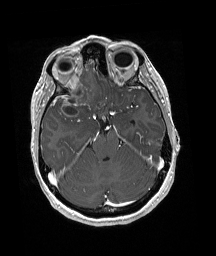
Brain MRI from a brain-tumour surgery series, one axial slice; position 124 of 192 along the scan axis; T1-weighted post-contrast; 1 mm slice thickness; 216 × 256 image matrix. From the clinical record (not read from this slice): histopathology: Oligodendroglioma; WHO grade: 3; IDH mutation: yes; tumour location: Right Frontal.
Annotated regions visible in this slice (expert manual segmentation):
- tumour: bounding box <53,74,97,117> (left, top, right, bottom; pixels)